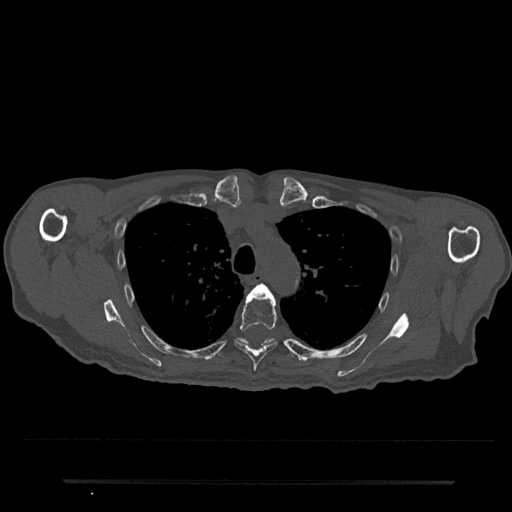
CT including the spine, one axial slice; slice 573 of 797 in the series (ordered by position); reconstruction kernel Br40s/3; 120 kVp; bone window (W 1800 / L 400 HU); 0.5 mm slice thickness; 512 × 512 image matrix, field of view 427 × 427 mm. Patient: male, 74 years. Case-level facts recorded for this patient, not image findings: primary cancer: prostate.
Annotated regions visible in this slice (semi-automatic segmentation, software-assisted and operator-edited):
- T4 vertebra: bounding box <251,283,268,294> (left, top, right, bottom; pixels)
- T5 vertebra: <234,289,278,371>
- T6 vertebra: <216,338,296,359>